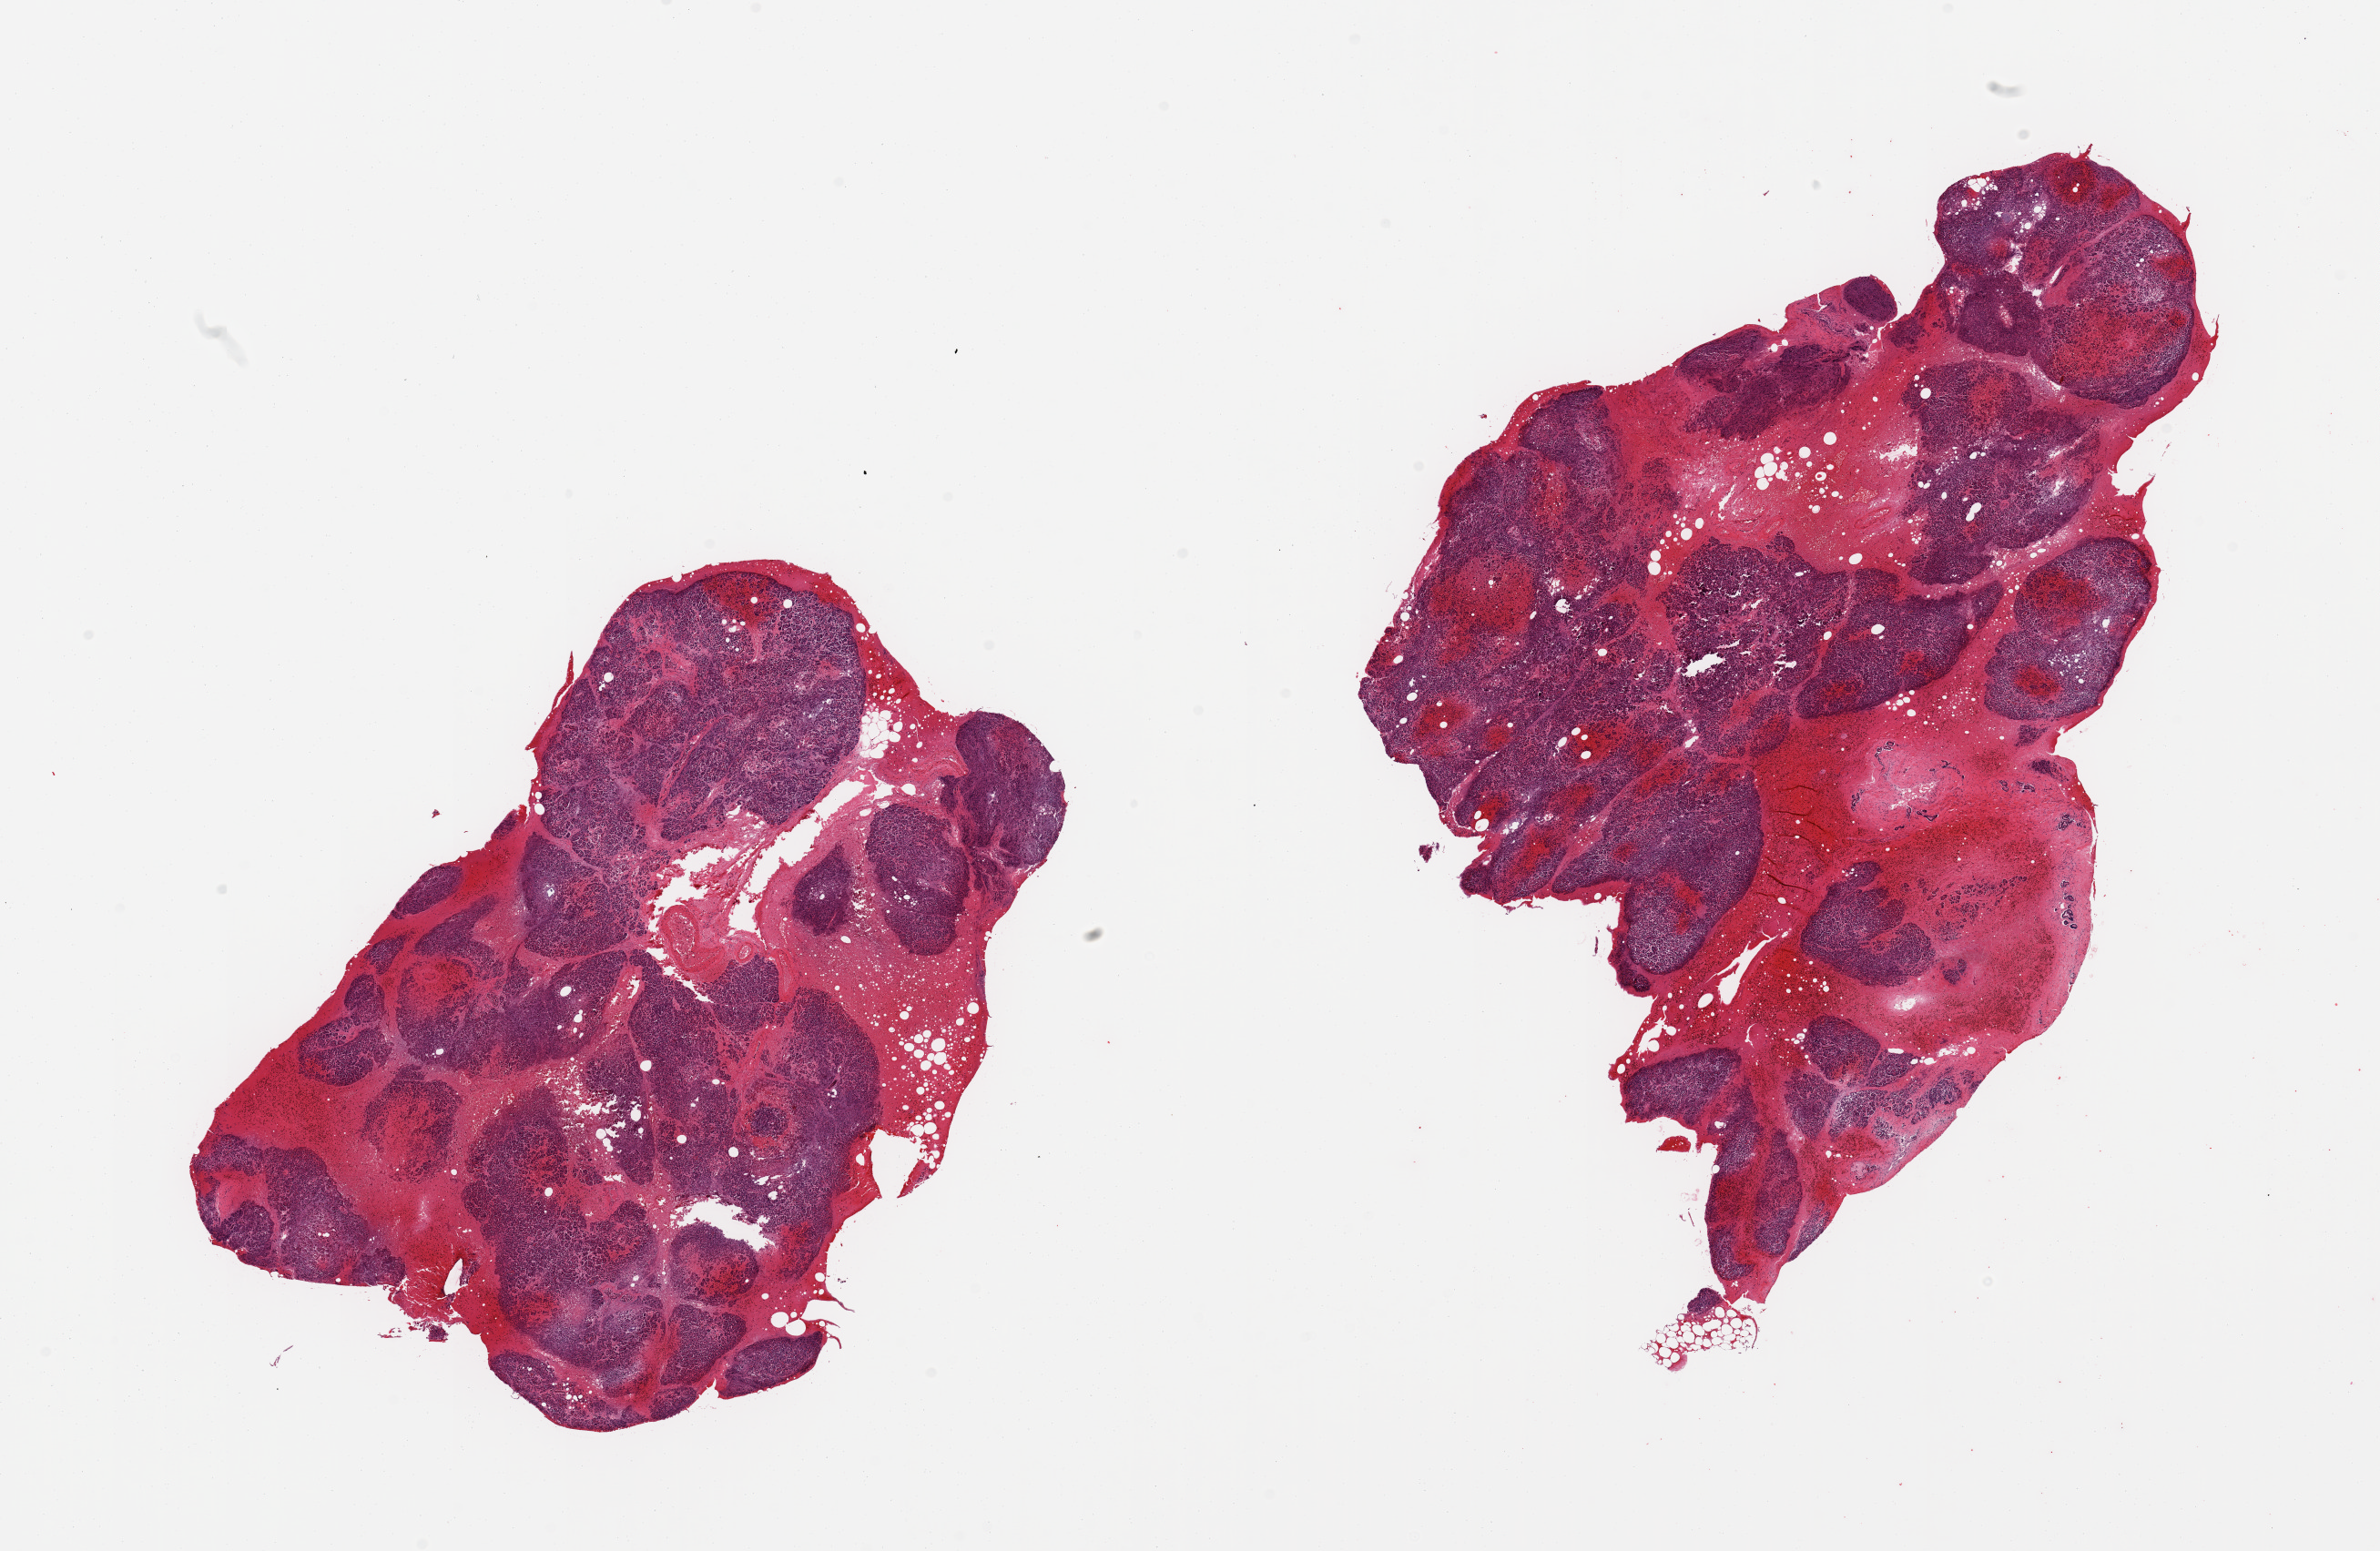
Haematoxylin and eosin whole-slide image, brightfield — a low-resolution overview of the entire scanned area, about 20.7 x 13.5 mm. PAXgene-fixed, paraffin-embedded tissue. Target tissue: pancreas. Donor tissue sample. Donor sex: male.
Pathologist's review note for this sample: 2 pieces, modarate-advanced saponification; Islets not well visualzied.